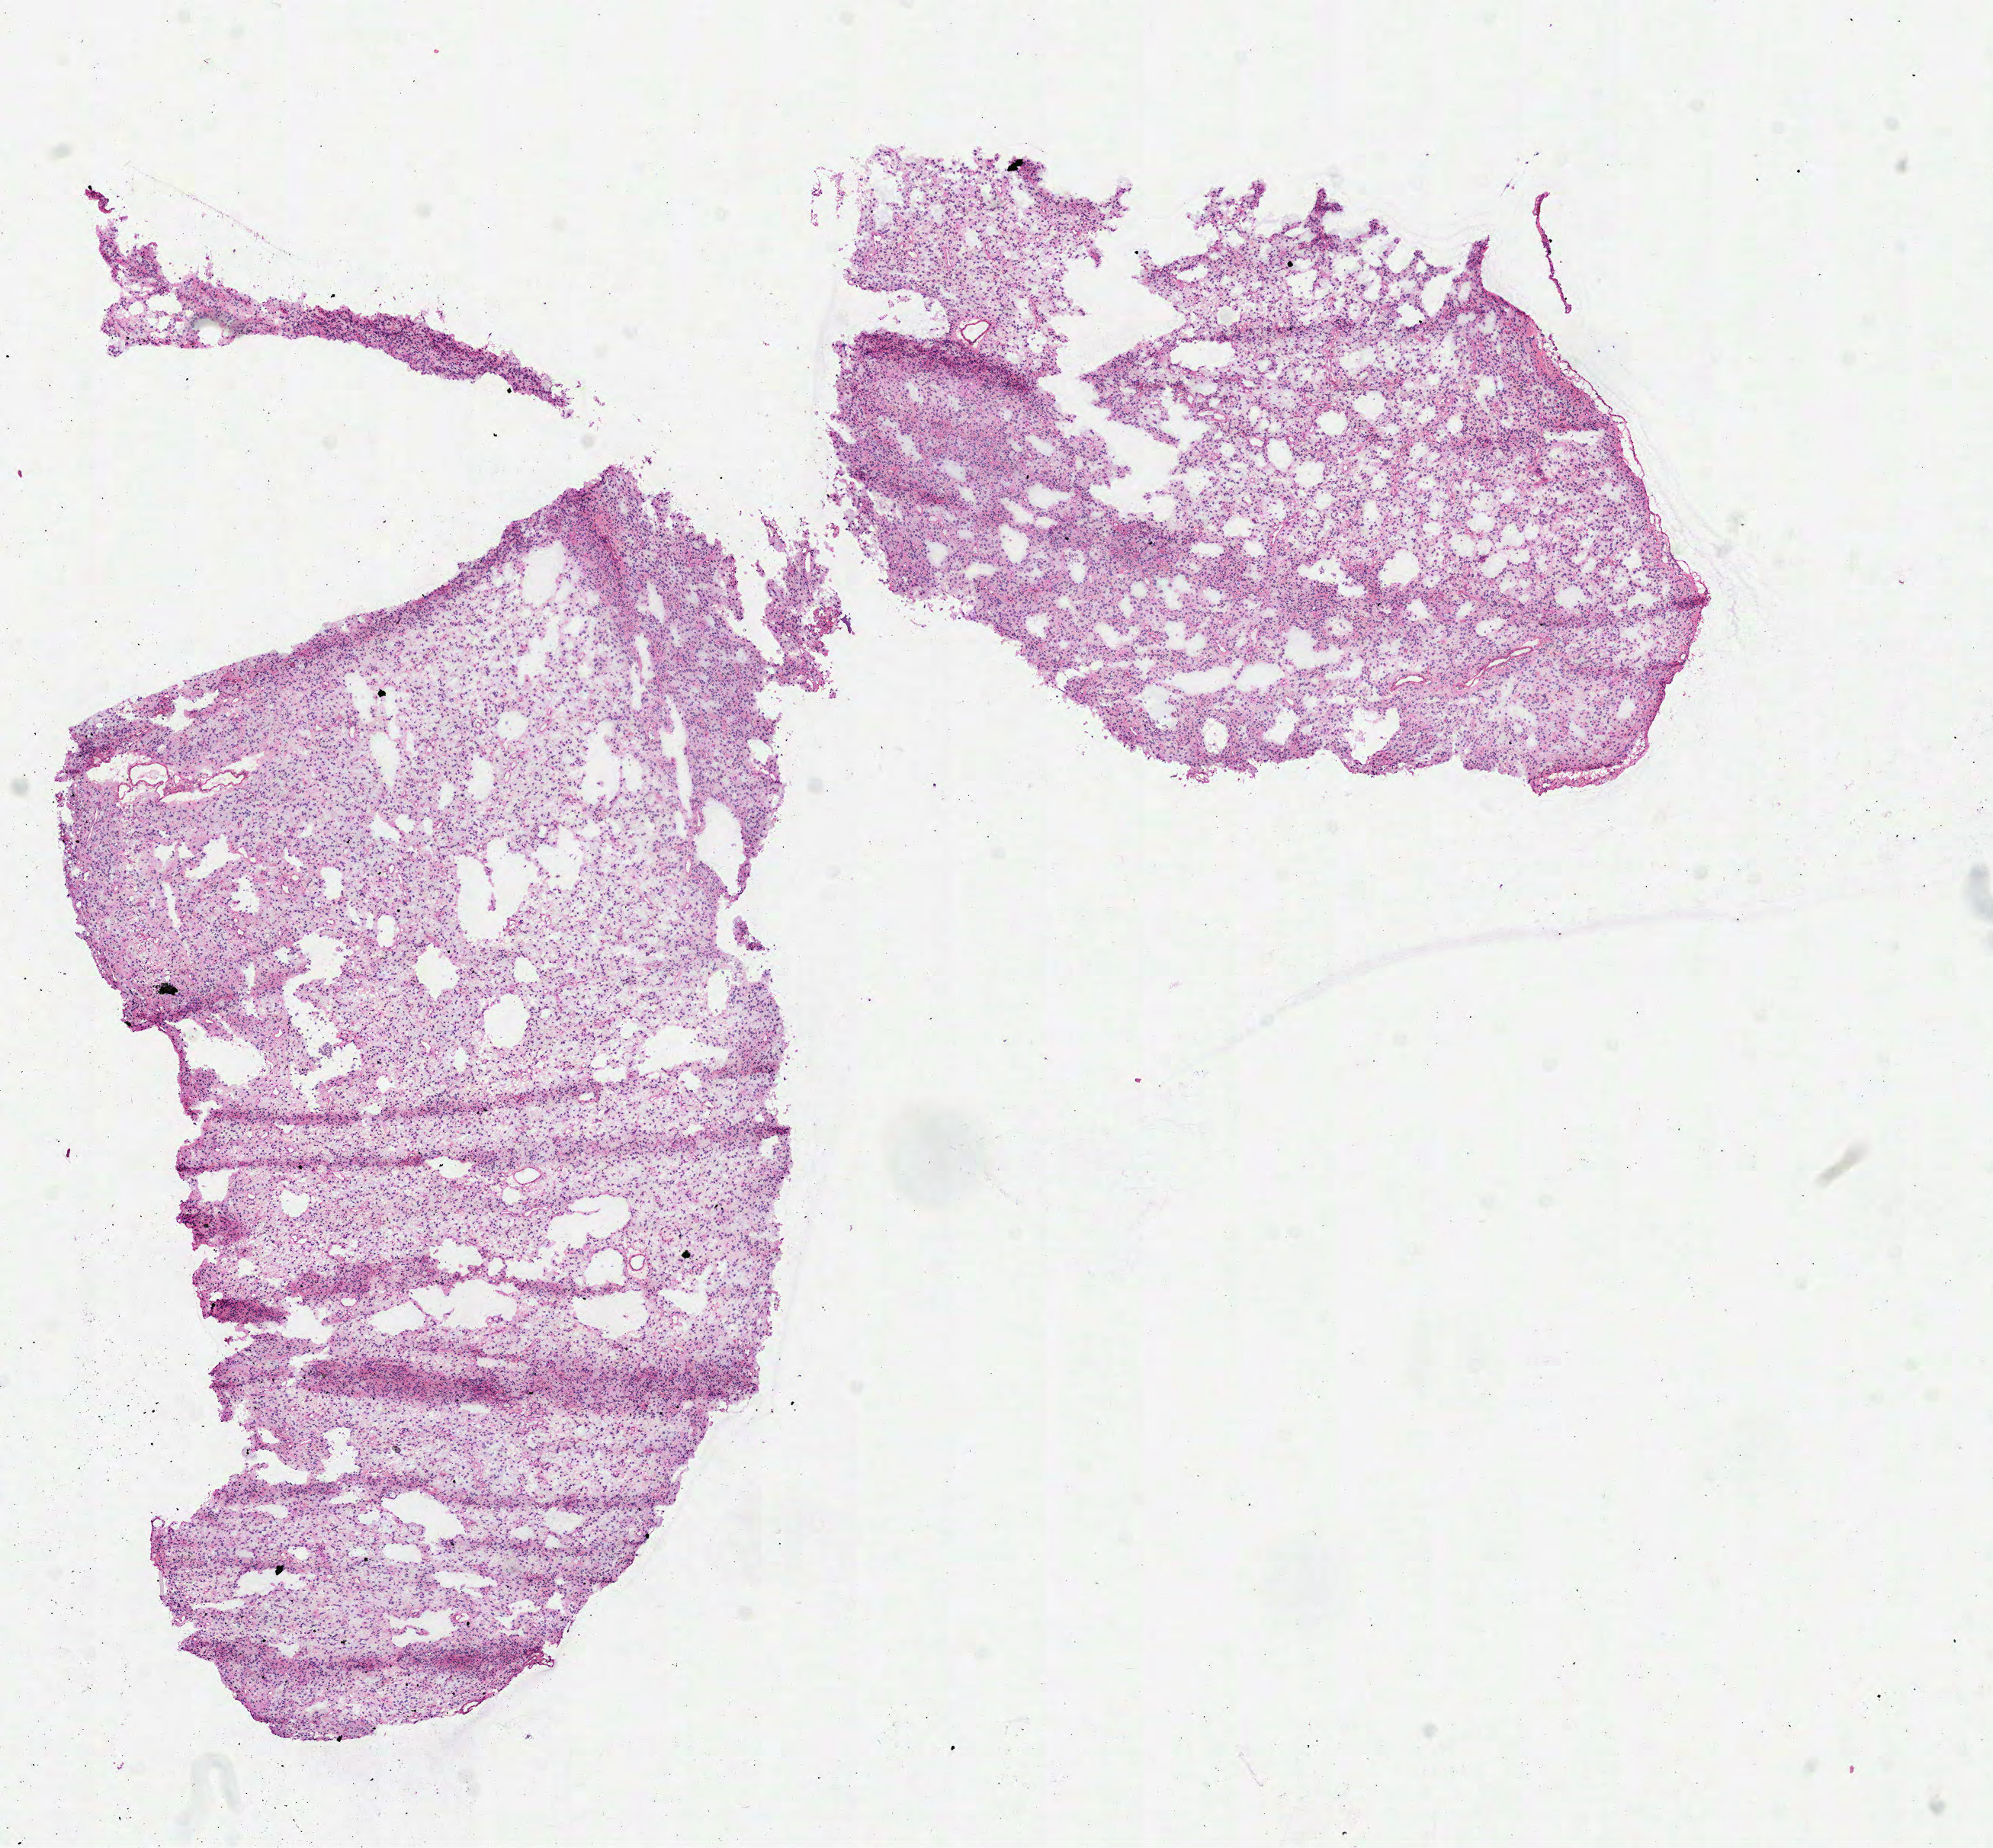
H&E-stained whole-slide image, whole scanned area (about 10.5 x 9.8 mm, slide scanned at 40x) shown as a low-resolution overview. Frozen section from the top of the tissue portion. Primary tumour sample from the brain. Male, age 37 years at initial diagnosis. Histologic grade: G3 (poorly differentiated). Slide review estimates, as recorded: tumour cells 100%, tumour nuclei 85%, normal cells 0%, stromal cells 0%, necrosis 0%.
Pathologic diagnosis: Astrocytoma, anaplastic (cerebrum).